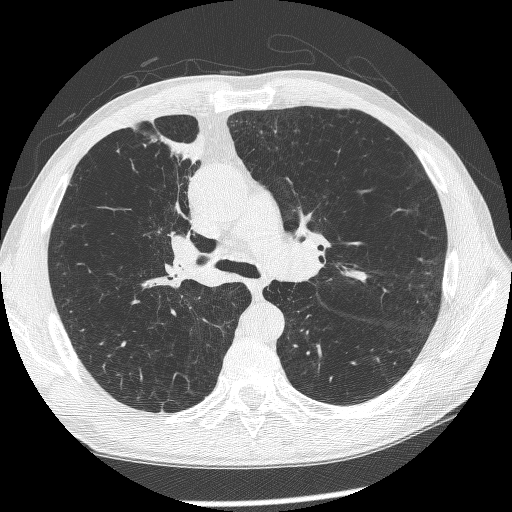
Low-dose screening chest CT, axial slice, first (baseline) screen, lung window (W 1500 / L -600 HU), 512 × 512 image matrix. Male, age 60 years at enrolment.
Expert-annotated lung lesion, box from (x=144, y=203) to (x=223, y=295) px. Reader record for this screening exam (exam-level; its link to the box is not recorded): non-calcified nodule or mass ≥4 mm, right upper lobe, 12 × 8 mm, spiculated (stellate) margins, mixed attenuation. Official screen result: positive, change unspecified: nodule(s) >= 4 mm or enlarging nodule(s), mass(es), or other non-specific abnormalities suspicious for lung cancer. Later outcome: lung cancer diagnosed 208 days after this screen — squamous cell carcinoma, NOS, right upper lobe, right middle lobe, right main stem bronchus, poorly differentiated (G3), stage IV (AJCC 6th edition).